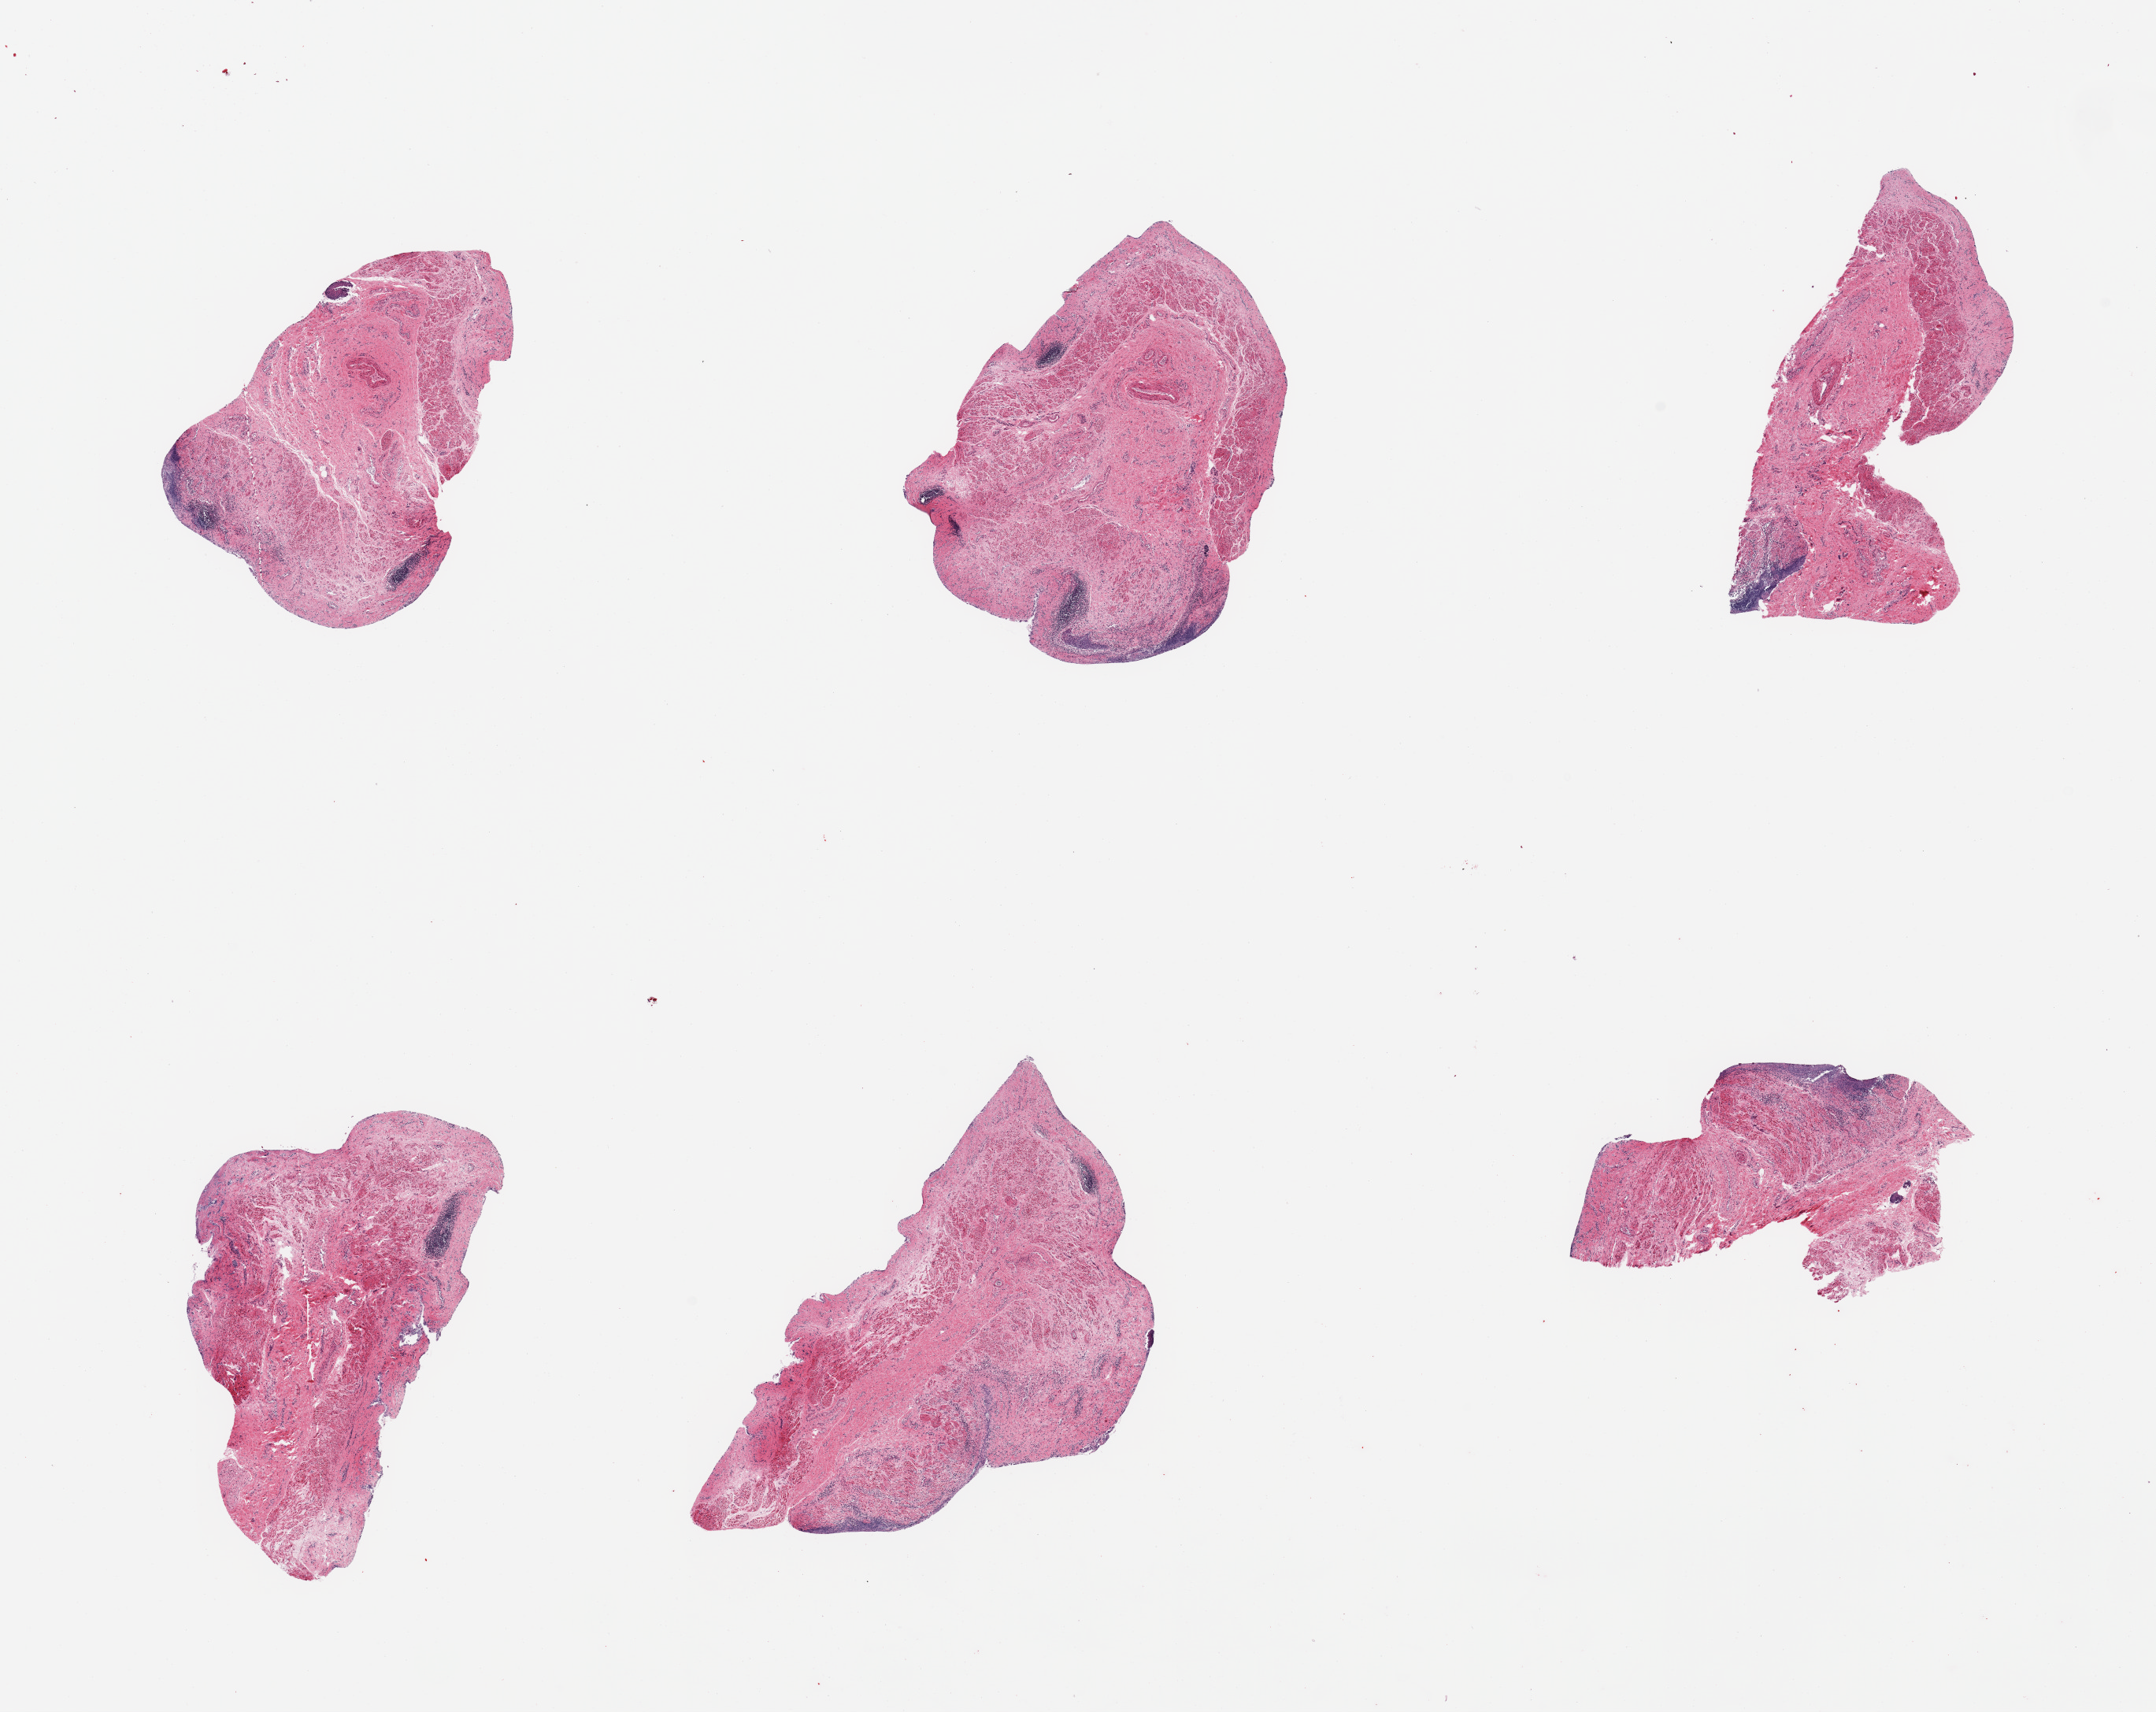
Digitized H&E-stained section, whole scanned area (about 21.7 x 17.2 mm, from a 20x scan) shown as a low-resolution overview; PAXgene-fixed, paraffin-embedded tissue; sampled site (target tissue): esophageal mucous membrane; tissue donor sample. Male donor.
- review note (as recorded): 6 pieces; essentially no intact epithelium